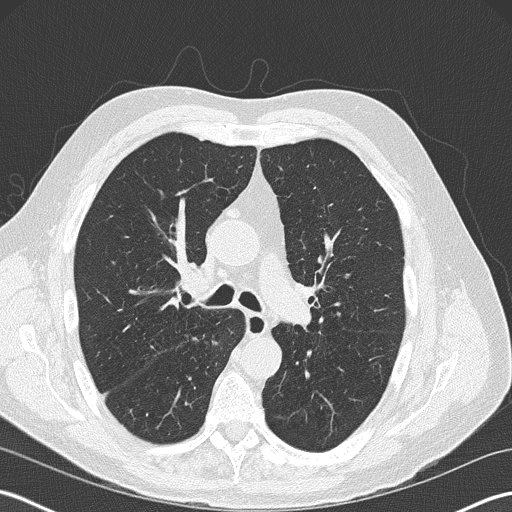
Low-dose screening chest CT, one axial slice. Slice 121 of 199 in the series (ordered by position). Reconstruction kernel B50f. 120 kVp. Lung window (W 1500 / L -600 HU). 512 × 512 image matrix, field of view 350 × 350 mm.
Structures marked on this image (outlined manually by an expert reader):
- lesion 1 (tumor, upper lobe of right lung): bounding box [x1, y1, x2, y2] px = [158, 357, 170, 366]